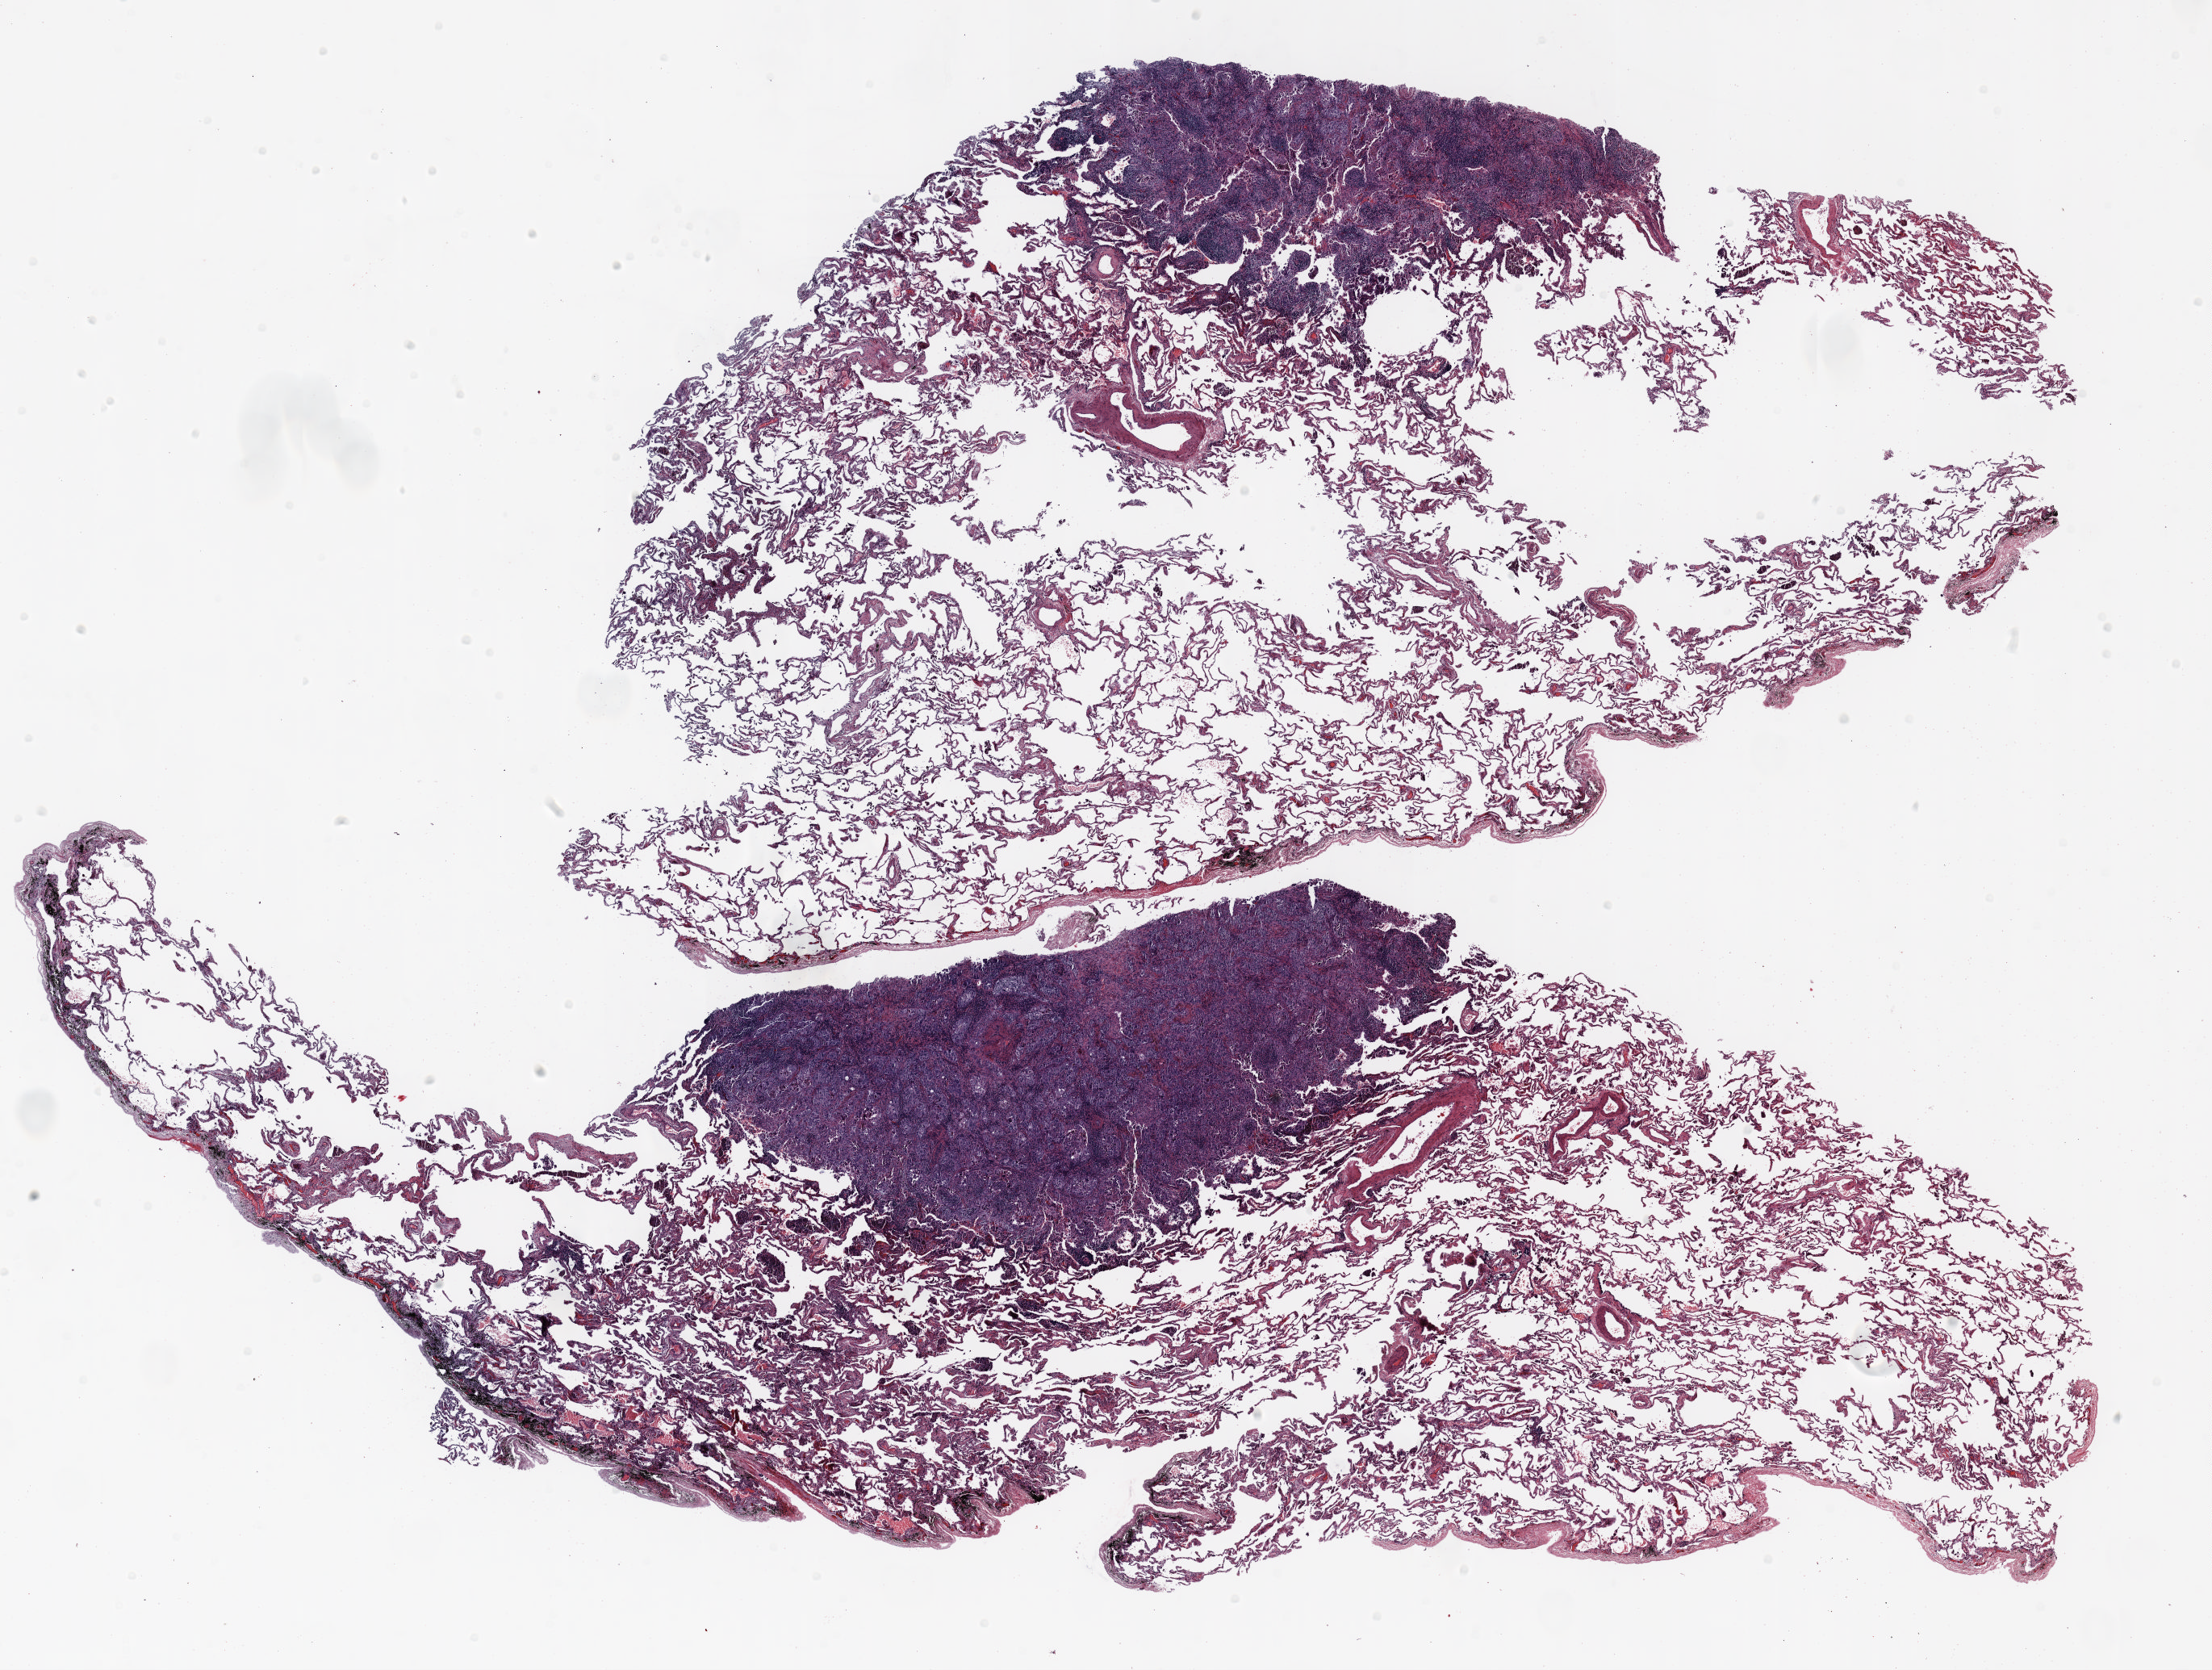
H&E-stained whole-slide image, shown as a low-resolution overview of the whole scanned area (about 22.0 x 16.6 mm, from a 20x scan). FFPE section. Lung tissue. Female, age 72 at enrolment. Current smoker at enrolment.
Participant's lung-cancer diagnosis: Non-small cell carcinoma.